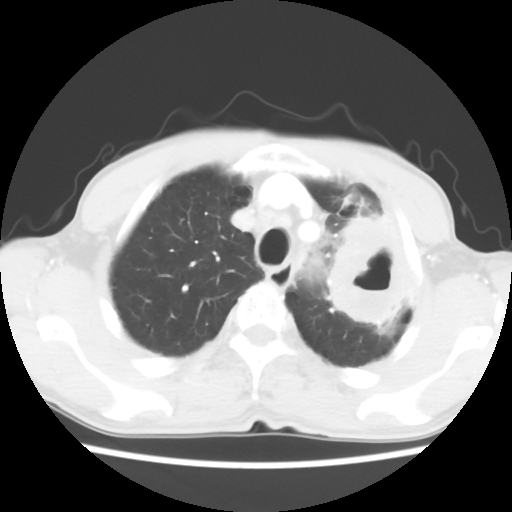
Chest CT, one axial slice; slice 48 of 60 in the series (ordered by position); 120 kVp; lung window (W 1500 / L -600 HU); 5 mm slice thickness; 512 × 512 image matrix, field of view 308 × 308 mm. Patient: male, 64 years. Case-level facts recorded for this patient, not image findings: clinical TNM (as recorded): T3 N3 M0; histopathological grade: G3.
Structures marked on this image (bounding box drawn by a radiologist):
- lung tumour (recorded histology: adenocarcinoma): bounding box [x1, y1, x2, y2] px = [315, 203, 418, 339]